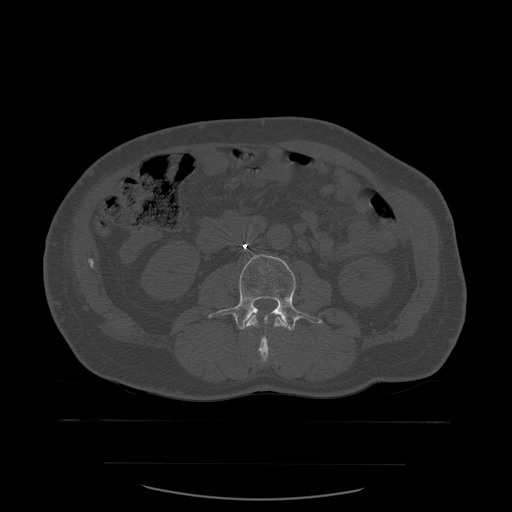
CT including the spine, one axial slice; slice 199 of 590 in the series (ordered by position); bone window (W 1800 / L 400 HU); 1.25 mm slice thickness; 512 × 512 image matrix, field of view 479 × 479 mm. Patient age 71 years. Case-level facts recorded for this patient, not image findings: primary cancer: lung.
Structures marked on this image (semi-automatically segmented with operator editing):
- L2 vertebra: box from (x=245, y=309) to (x=291, y=363) px
- L3 vertebra: (x=209, y=254)–(x=324, y=331)